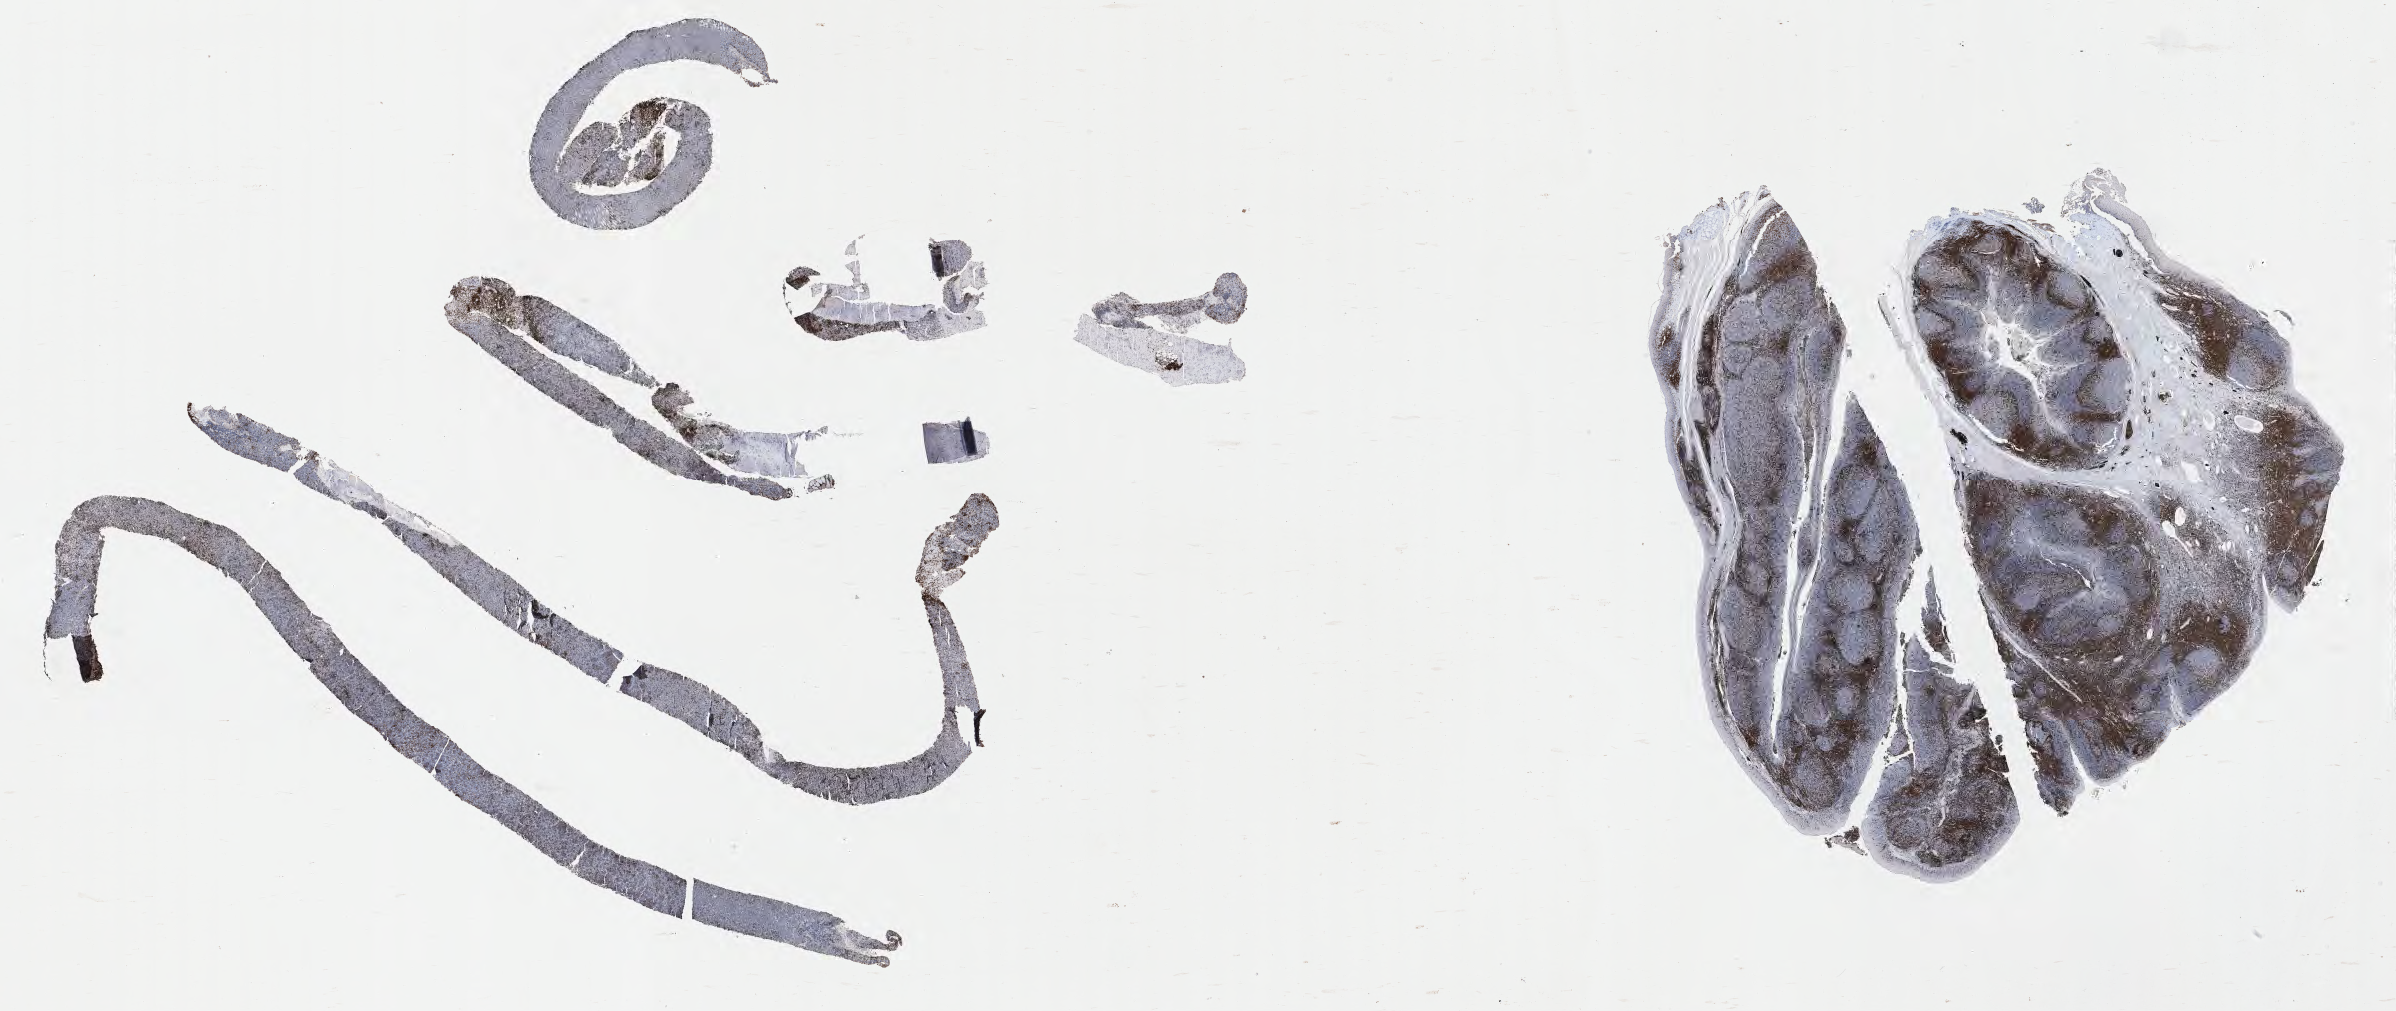
IHC for CD3, whole-slide image — shown as a low-resolution overview of the whole scanned area (about 38.8 x 16.4 mm), tumor tissue. Patient: male, 45 years old.
Diagnosis: Burkitt lymphoma, NOS.